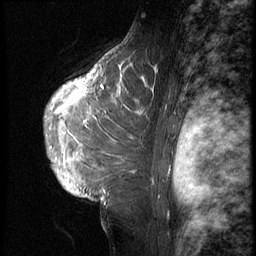
Breast MRI (dynamic contrast-enhanced), one sagittal slice. Slice 43 of 62 in the series (ordered by position). 3 images stored at this slice position (order not interpretable as contrast timing). 1.5 T. TE 4.2 ms, TR 9 ms. 2.5 mm slice thickness. 256 × 256 image matrix. Patient: female, 28 years. Case-level facts recorded for this patient, not image findings: setting: breast cancer imaged before/during neoadjuvant chemotherapy.
Annotated regions visible in this slice (semi-automatically segmented with operator editing):
- analysis volume of interest (the breast-tissue region the enhancement analysis was run in; not a lesion): bounding box (x1, y1, x2, y2) in pixels: (43, 45, 192, 207)
- tumour enhancement mask (voxels above the 140 % enhancement threshold inside the analysis volume of interest): (55, 62, 192, 185)